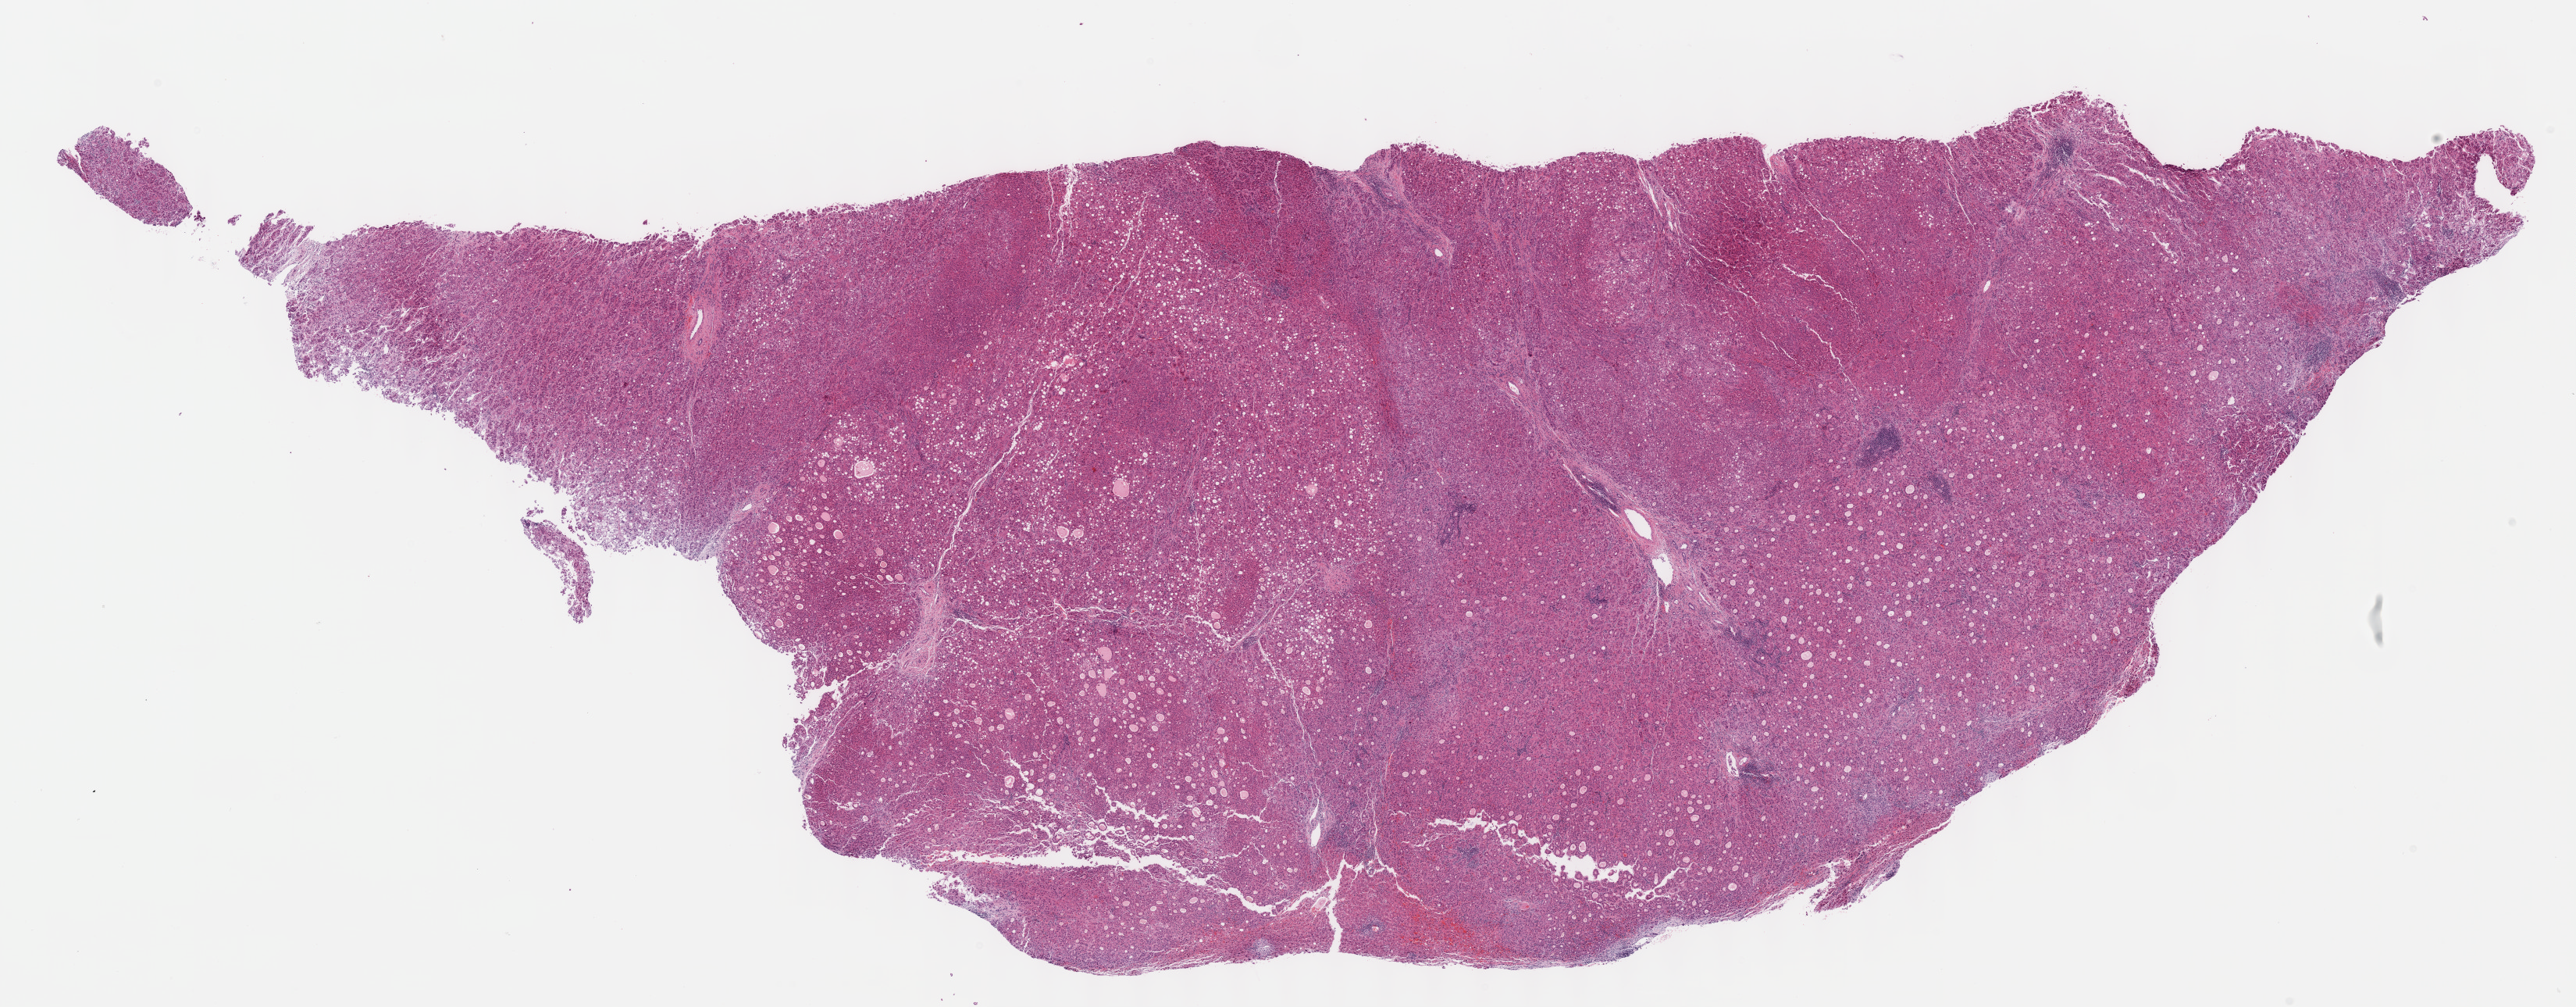
Digitized H&E tissue section (whole slide) — low-resolution overview of the scanned area, about 26.7 x 10.4 mm; formalin-fixed paraffin-embedded (FFPE) diagnostic section; primary tumour sample from the liver. Male, age 43 years at initial diagnosis. Histologic grade: G2 (moderately differentiated).
Diagnosis: Hepatocellular carcinoma, NOS. AJCC pathologic stage: I.